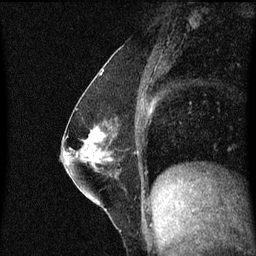
Breast MRI (dynamic contrast-enhanced), one sagittal slice; slice 25 of 60 in the series (ordered by position); dynamic contrast-enhanced series, image 2 of 3 at this slice position (ordered by acquisition); 1.5 T; TE 4.2 ms, TR 8.4 ms; 2 mm slice thickness; 256 × 256 image matrix, field of view 200 × 200 mm. Female patient, age 52 years. Case-level facts recorded for this patient, not image findings: setting: breast cancer imaged before/during neoadjuvant chemotherapy; receptor status: HER2-positive.
Structures marked on this image (semi-automatic segmentation, software-assisted and operator-edited):
- analysis volume of interest (the breast-tissue region the enhancement analysis was run in; not a lesion): box from (x=71, y=118) to (x=121, y=187) px
- tumour enhancement mask (voxels above the 70 % enhancement threshold inside the analysis volume of interest): (x=90, y=130)–(x=99, y=139)